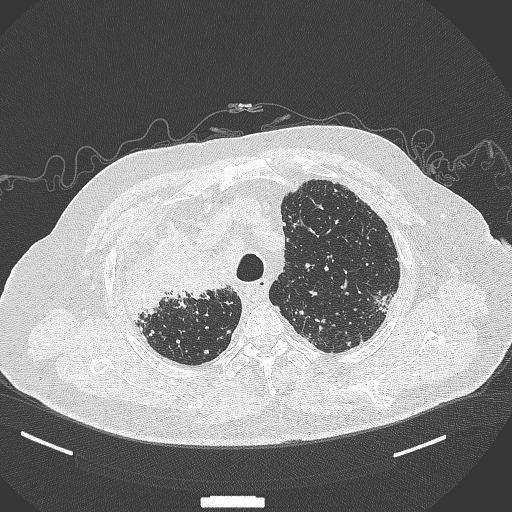
Chest CT, one axial slice; 120 kVp; lung window (W 1500 / L -600 HU); 512 × 512 image matrix, field of view 400 × 400 mm. Patient: male, 69 years. From the clinical record (not read from this slice): clinical TNM (as recorded): T4 N3 M1.
Structures marked on this image (bounding box drawn by a radiologist):
- lung tumour (recorded histology: adenocarcinoma): box from (x=125, y=220) to (x=225, y=314) px